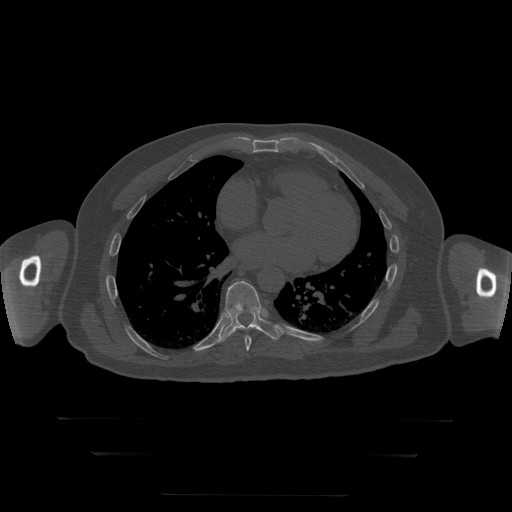
CT including the spine, one axial slice. Position 151 of 397 along the scan axis. Reconstruction kernel STANDARD. 120 kVp. Bone window (W 1800 / L 400 HU). 1.25 mm slice thickness. 512 × 512 image matrix. Patient age 73 years. Case-level facts recorded for this patient, not image findings: primary cancer: prostate.
Structures marked on this image (semi-automatic segmentation, software-assisted and operator-edited):
- T8 vertebra: bounding box (x1, y1, x2, y2) in pixels: (245, 335, 252, 351)
- T9 vertebra: (220, 281, 283, 343)